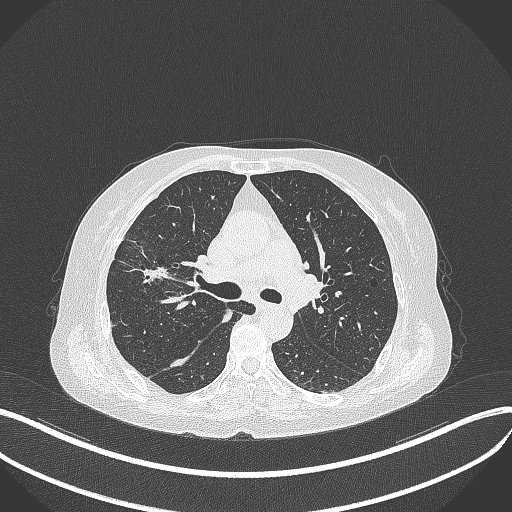
Chest CT, one axial slice. Slice 253 of 429 in the series (ordered by position). Reconstruction kernel B70f. 120 kVp. Lung window (W 1500 / L -600 HU). 1 mm slice thickness. 512 × 512 image matrix, field of view 400 × 400 mm. Patient: female, 69 years. Case-level facts recorded for this patient, not image findings: clinical TNM (as recorded): T1b N3 M0.
Annotated regions visible in this slice (bounding box drawn by a radiologist):
- lung tumour (recorded histology: small cell carcinoma): bounding box <123,257,174,286> (left, top, right, bottom; pixels)